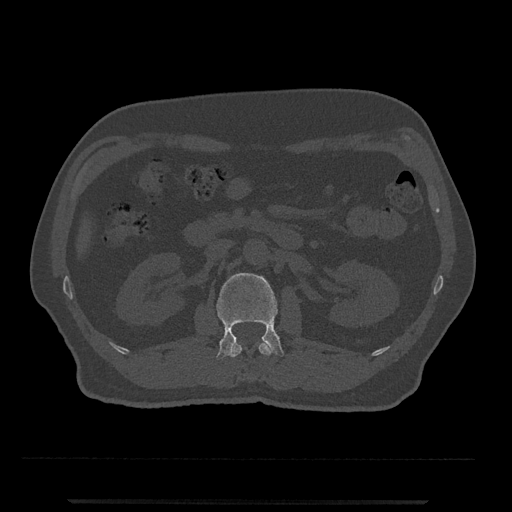
CT including the spine, one axial slice. Position 288 of 797 along the scan axis. 120 kVp. Bone window (W 1800 / L 400 HU). 0.5 mm slice thickness. 512 × 512 image matrix, field of view 419 × 419 mm. Patient: male, 63 years. From the clinical record (not read from this slice): primary cancer: prostate.
Structures marked on this image (semi-automatic segmentation, software-assisted and operator-edited):
- L1 vertebra: bounding box [x1, y1, x2, y2] px = [231, 341, 273, 357]
- L2 vertebra: [216, 273, 284, 359]